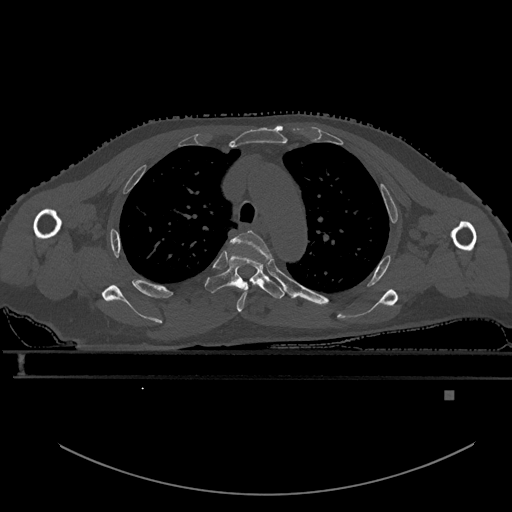
CT including the spine, one axial slice; slice 421 of 969 in the series (ordered by position); bone window (W 1800 / L 400 HU); 512 × 512 image matrix, field of view 456 × 456 mm. Patient: male, 82 years. Case-level facts recorded for this patient, not image findings: primary cancer: prostate; vertebrae with lytic lesions (as recorded): T11, T9, T8, T2.
Outlined on this slice (semi-automatic segmentation, software-assisted and operator-edited):
- T3 vertebra: bounding box [x1, y1, x2, y2] px = [232, 230, 272, 312]
- T4 vertebra: [205, 255, 285, 299]